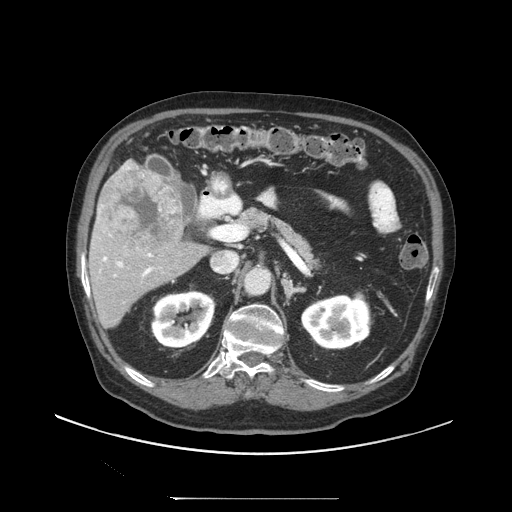
Contrast-enhanced abdominal CT (liver protocol), one axial slice. Position 52 of 97 along the scan axis. Reconstruction kernel STANDARD. 140 kVp. Soft-tissue window (W 400 / L 40 HU). 2.5 mm slice thickness. 512 × 512 image matrix, field of view 450 × 450 mm. From the clinical record (not read from this slice): diagnosis: hepatocellular carcinoma (patient treated with transarterial chemoembolisation; whether this scan precedes or follows treatment is not stated here); TNM stage (as recorded): Stage-IIIC; Child-Pugh class: A; tumour differentiation: well differentiated; tumour nodularity: uninodular.
Structures marked on this image (semi-automatically segmented with operator editing):
- liver parenchyma outside the tumour (the mass and vessels are separate outlines, so this box may not span the whole liver): bounding box (x1, y1, x2, y2) in pixels: (88, 160, 207, 328)
- mass: (101, 168, 183, 256)
- liver vessels: (98, 165, 154, 277)